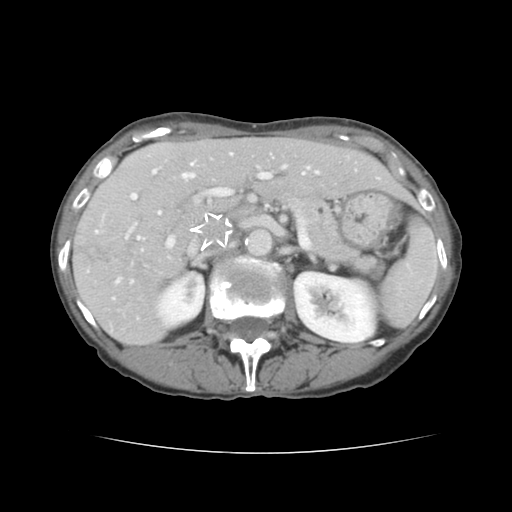
Contrast-enhanced abdominal CT, one axial slice. Position 81 of 136 along the scan axis. Intravenous contrast given. Soft-tissue window (W 400 / L 40 HU). 2.5 mm slice thickness. 512 × 512 image matrix. Female patient, age 77 years. From the clinical record (not read from this slice): diagnosis: colorectal cancer liver metastases, imaged before liver resection; multiple liver metastases: yes; largest metastasis: 3 cm; disease in both lobes: no.
Structures marked on this image (outlined manually by an expert reader):
- hepatic veins: bounding box <138,163,318,239> (left, top, right, bottom; pixels)
- liver: <74,137,410,345>
- planned liver remnant (the part of the liver to remain after resection): <154,137,410,209>
- portal vein (with intrahepatic branches): <96,165,285,282>